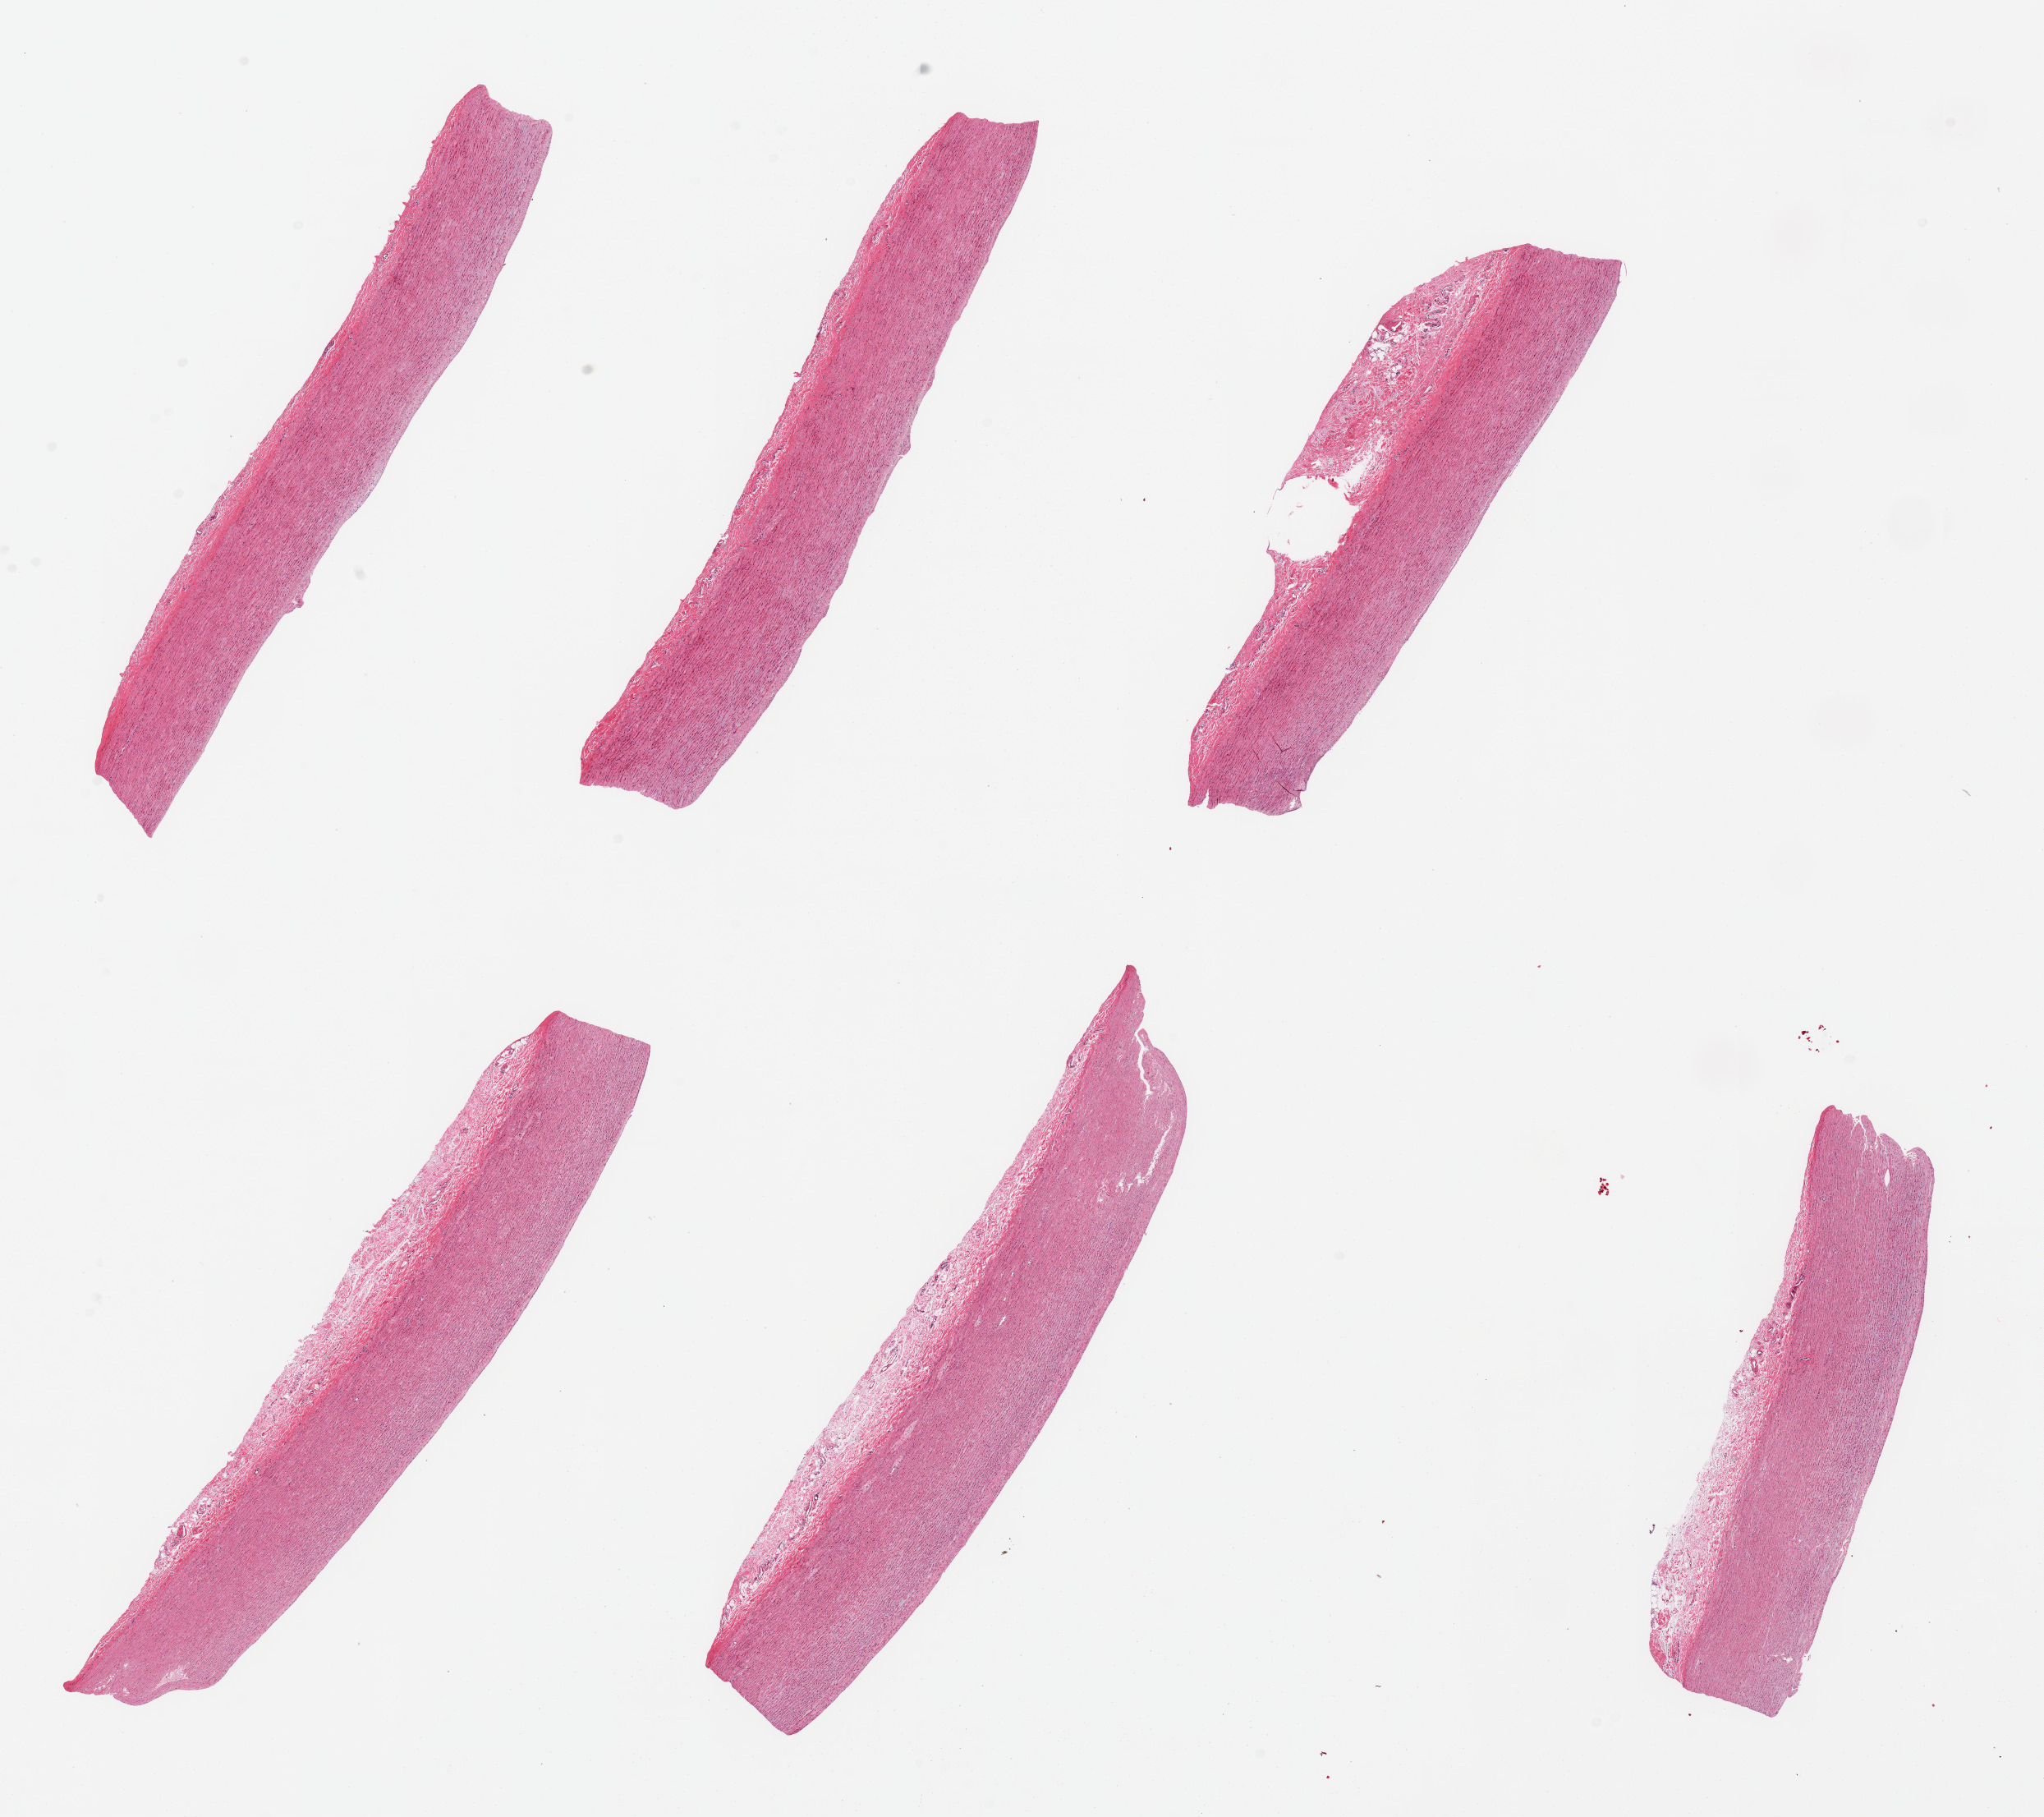
Whole-slide image, H&E stain, whole scanned area (about 19.7 x 17.5 mm) shown as a low-resolution overview. PAXgene-fixed, paraffin-embedded tissue. Section of esophageal muscle (target tissue). Tissue donor sample.
- reviewer comment on this tissue sample: 6 pieces, sections of large elastic artery c/w aorta, not esophageal muscularis